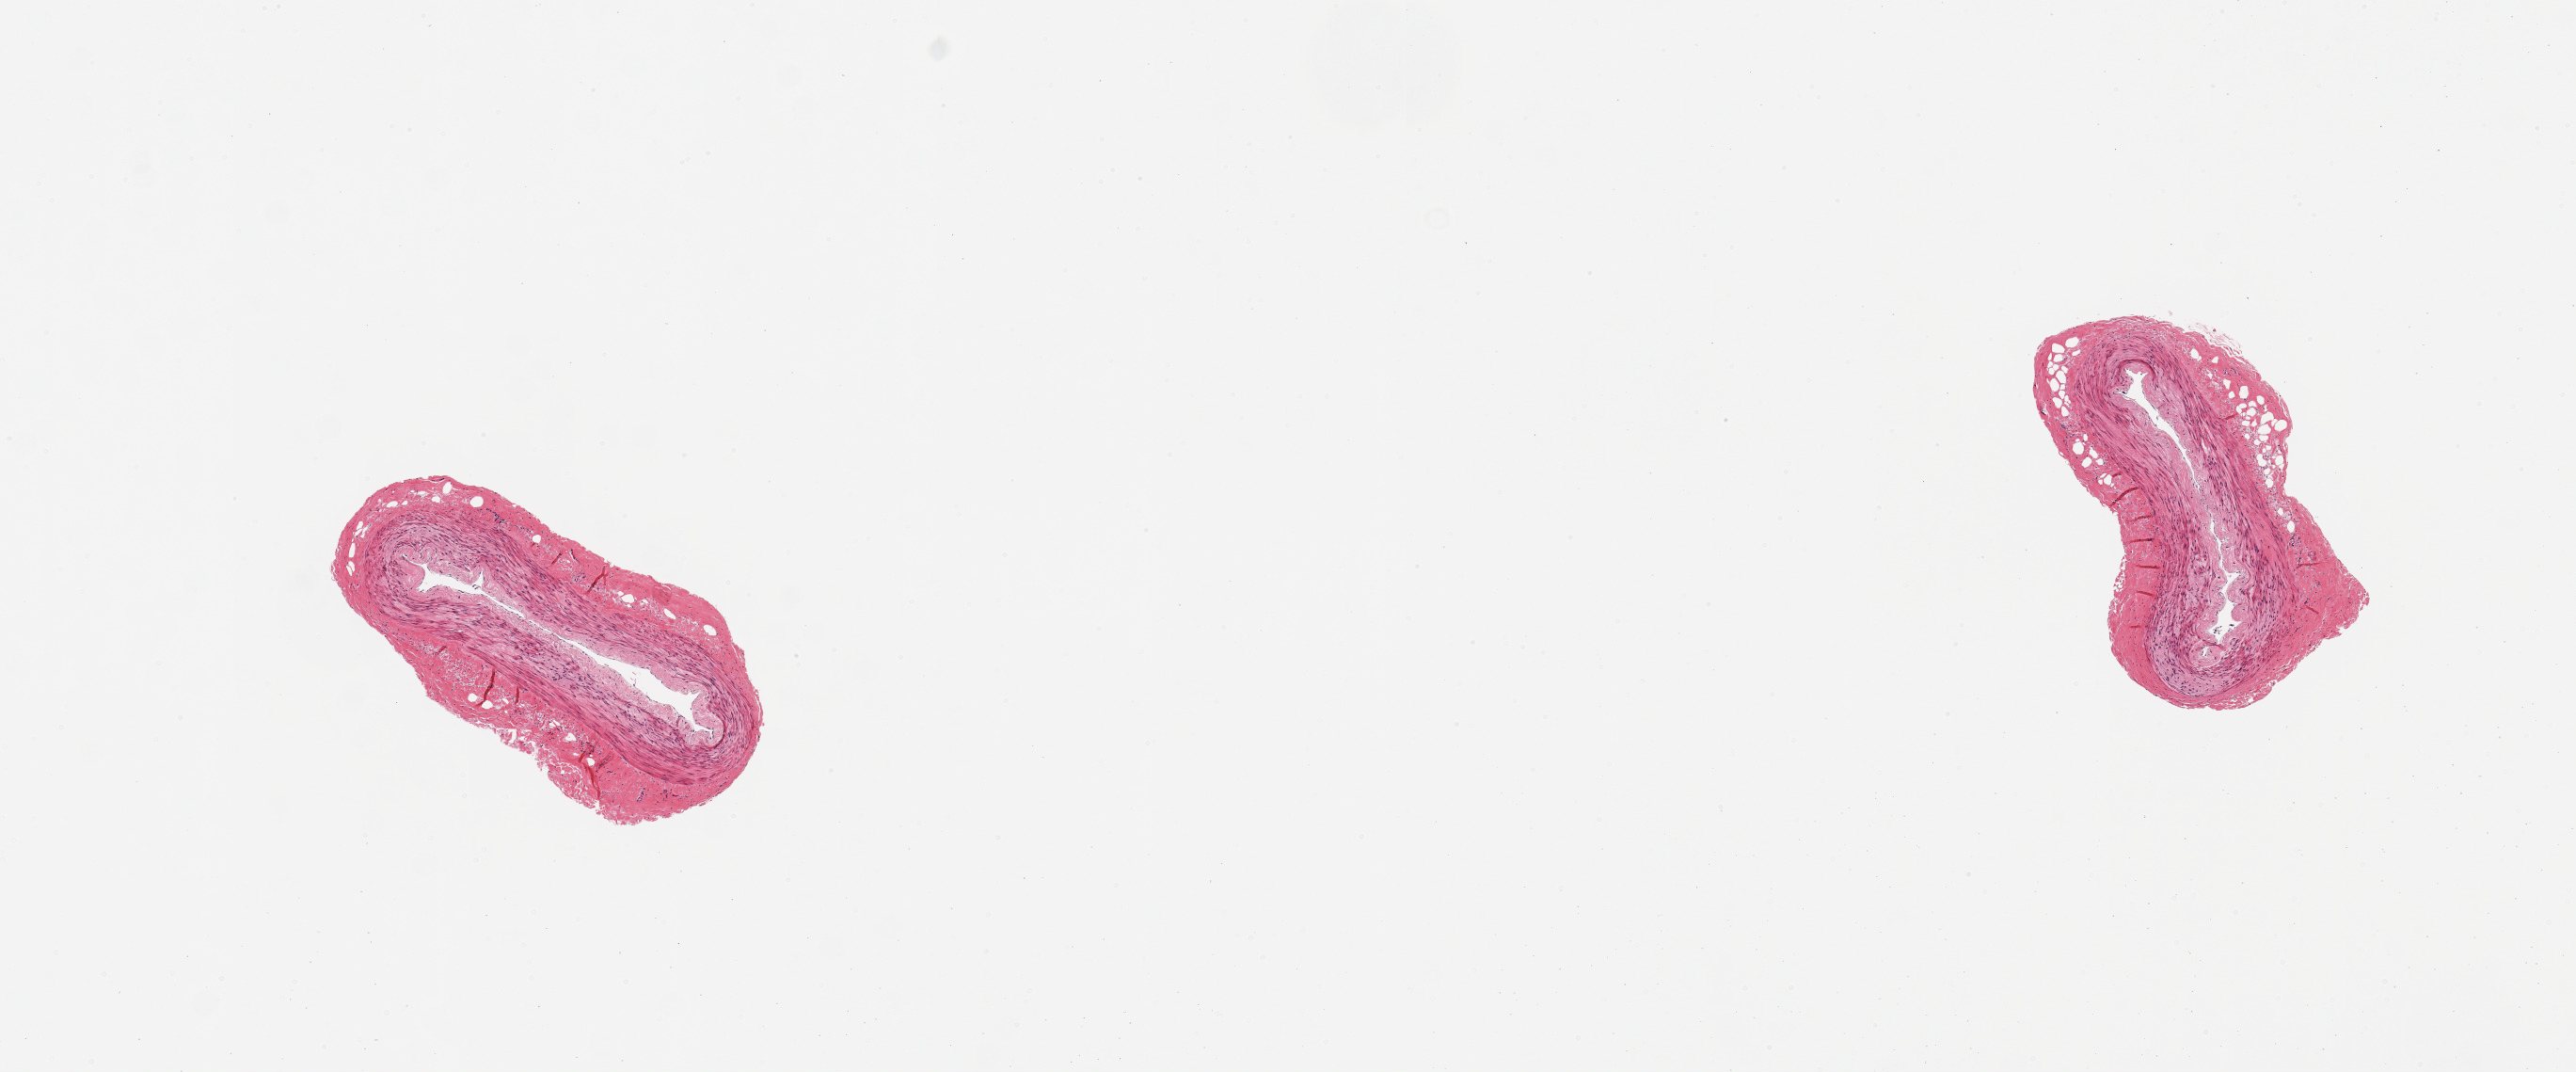
Hematoxylin and eosin (H&E) whole-slide image — low-resolution overview of the scanned area, about 10.8 x 4.5 mm; PAXgene-fixed paraffin-embedded (PFPE) section; section of tibial artery (target tissue); donor tissue sample. Donor: female.
Reviewer comment on this tissue sample: 2 pieces; no lesions; well trimmed.